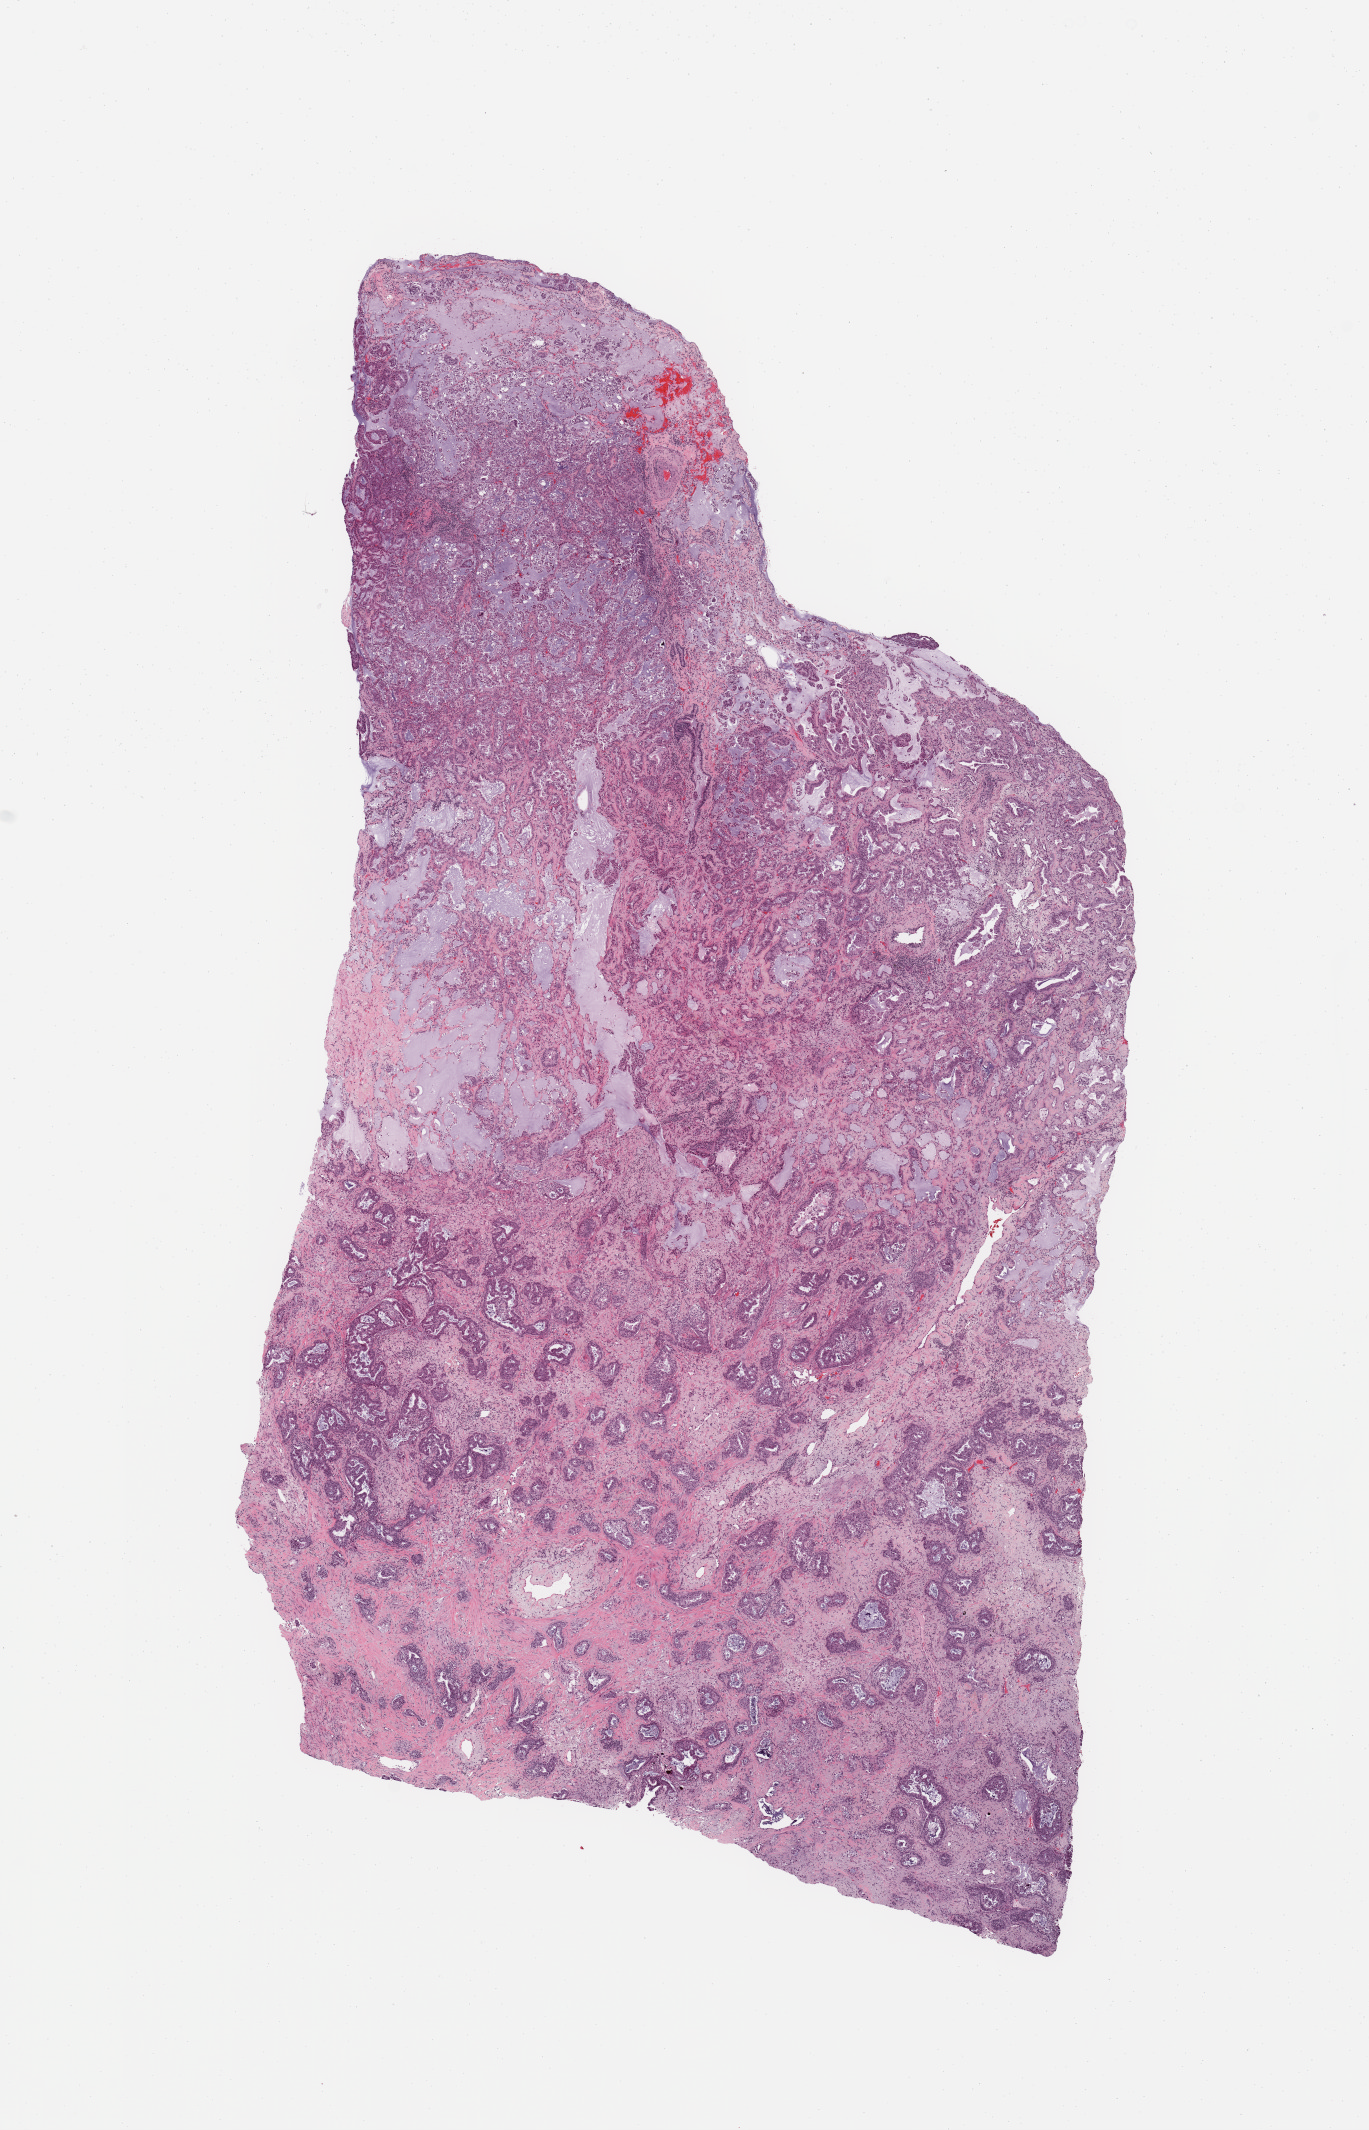
Whole-slide histology image, H&E-stained, whole scanned area (about 10.8 x 16.8 mm, slide scanned at 20x) shown as a low-resolution overview; tumour tissue sample, sampled site: lung. 60-year-old female patient. Histologic grade: G3 (poorly differentiated). Pathologist review of this section (percent, as recorded): tumour nuclei 65%, necrosis 2%.
• primary tumour site (as recorded): right upper lobe
• histologic diagnosis: Adenocarcinoma, NOS
• AJCC pathologic stage: IIA